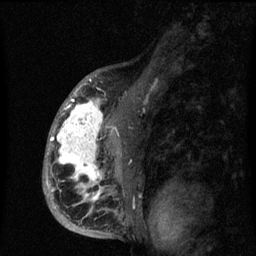
Breast MRI (dynamic contrast-enhanced), one sagittal slice. Position 42 of 60 along the scan axis. Dynamic contrast-enhanced series, image 2 of 3 at this slice position (ordered by acquisition). 1.5 T. TE 4.2 ms, TR 8 ms. 2 mm slice thickness. 256 × 256 image matrix. Patient: female, 50 years.
Outlined on this slice (semi-automatic segmentation, software-assisted and operator-edited):
- analysis volume of interest (the breast-tissue region the enhancement analysis was run in; not a lesion): bounding box <43,90,141,216> (left, top, right, bottom; pixels)
- tumour enhancement mask (voxels above the 70 % enhancement threshold inside the analysis volume of interest): <46,90,119,201>